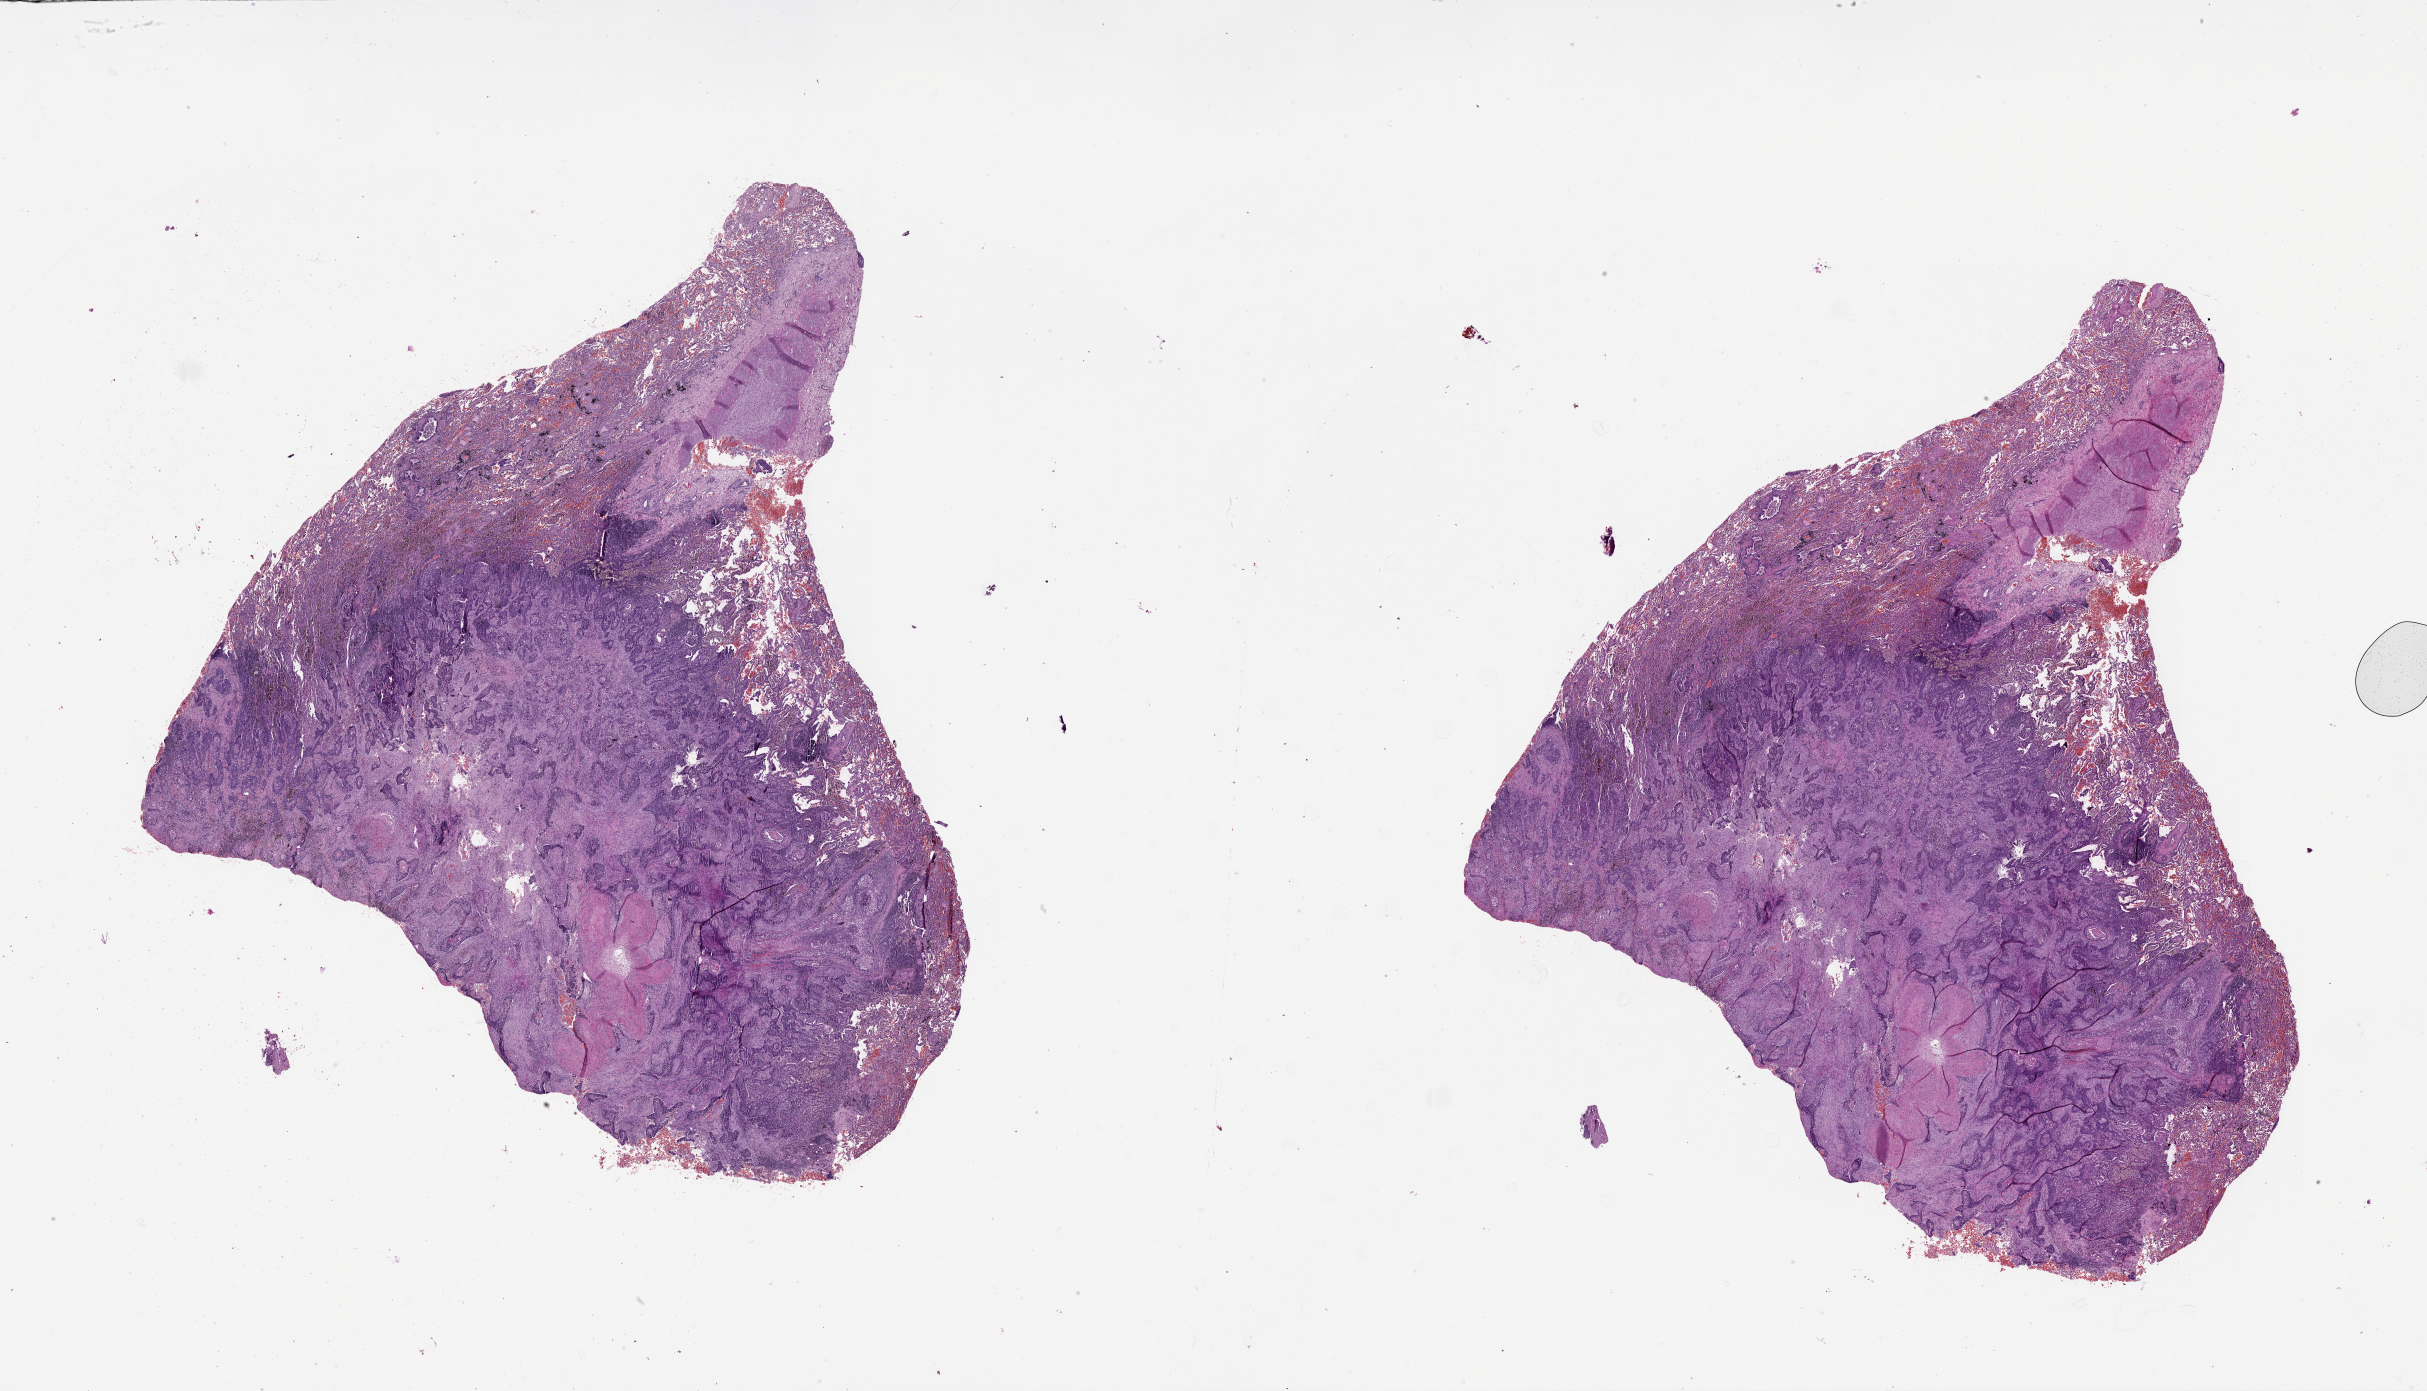
Digitized H&E-stained tissue section (whole slide), a low-resolution overview of the entire scanned area, about 39.1 x 22.4 mm; tumour tissue sample, lung. Male, 49 y/o.
Patient diagnosis (cohort enrolment): squamous cell carcinoma (lung).